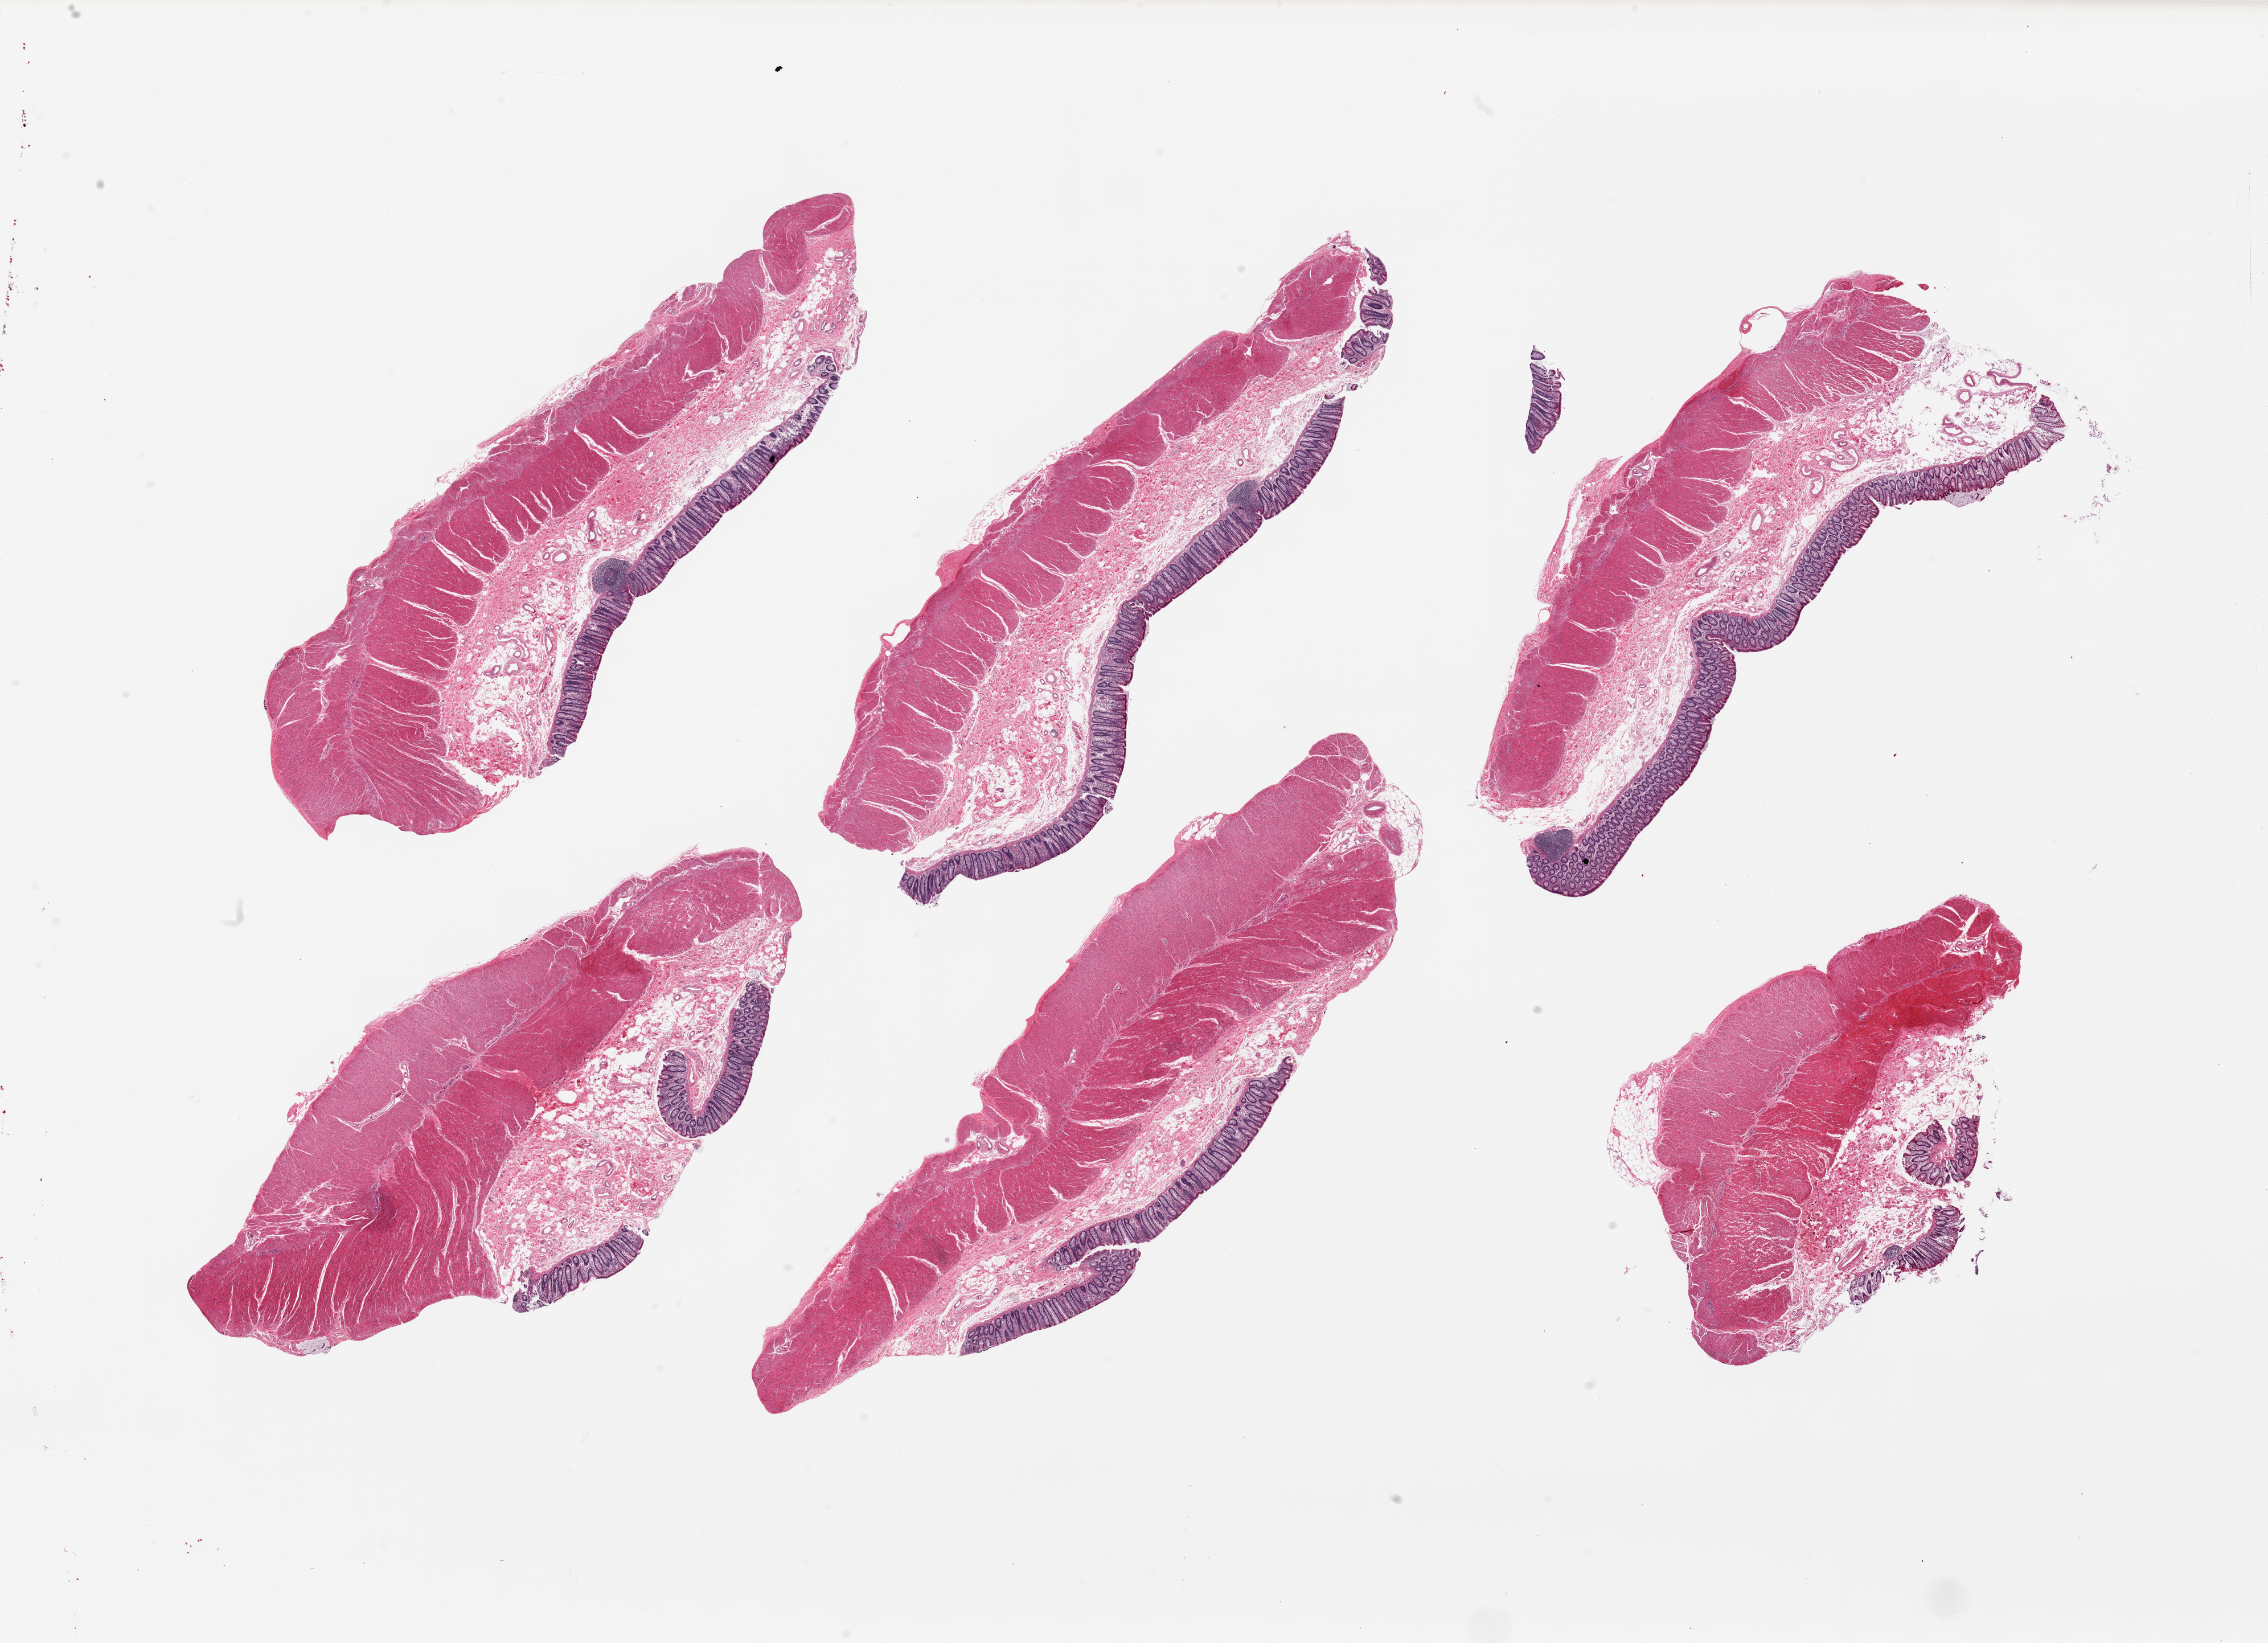
Whole-slide image, H&E stain, brightfield — low-resolution overview of the scanned area, about 31.5 x 22.8 mm. PAXgene-fixed paraffin-embedded (PFPE) section. Section of transverse colon (target tissue). Donor tissue sample. Donor: male.
• pathologist's review note for this sample: 6 pieces, up to 12x4.5mm; mucosa well preserved, ~15% of thickness